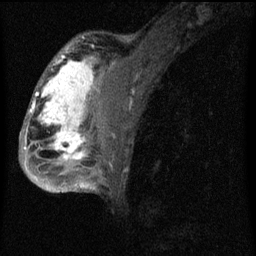
Breast MRI (dynamic contrast-enhanced), one sagittal slice; dynamic contrast-enhanced series, image 2 of 4 at this slice position (ordered by acquisition); 1.5 T; TE 4.2 ms, TR 8 ms; 2 mm slice thickness; 256 × 256 image matrix. Patient: female, 50 years.
Annotated regions visible in this slice (semi-automatic segmentation, software-assisted and operator-edited):
- analysis volume of interest (the breast-tissue region the enhancement analysis was run in; not a lesion): box from (x=26, y=44) to (x=124, y=177) px
- tumour enhancement mask (voxels above the 70 % enhancement threshold inside the analysis volume of interest): (x=26, y=46)–(x=95, y=161)